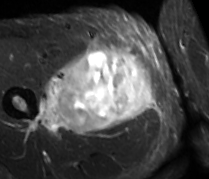
MRI of an extremity soft-tissue mass, one axial slice; position 37 of 89 along the scan axis; STIR; MR volume resampled by the dataset authors to the PET/CT grid (not the native acquisition matrix); 3.27 mm slice thickness; 209 × 179 image matrix. Male patient. From the clinical record (not read from this slice): histological type: undifferentiated - pleiomorphic; grade: high; site of the primary tumour: right thigh.
Annotated regions visible in this slice (expert contour drawn on MRI and transferred to this co-registered scan by the dataset authors):
- gross tumour volume including surrounding oedema: bounding box (x1, y1, x2, y2) in pixels: (34, 44, 154, 134)
- gross tumour volume (mass): (57, 44, 154, 134)